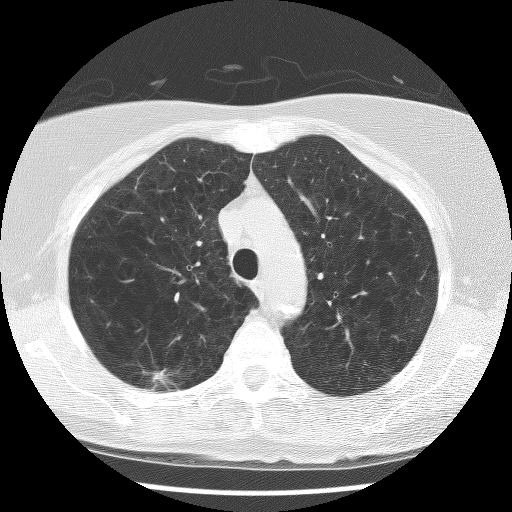
Chest CT (low-dose screening protocol), one axial image, first (baseline) screen, lung window (W 1500 / L -600 HU), 2.5 mm slice thickness, lung (sharp) reconstruction kernel (BONE), 120 kVp, 512 × 512 image matrix, field of view 310 × 310 mm. Female participant, aged 63 years at enrolment.
Expert-annotated lung lesion, bounding box <130,353,190,403> (left, top, right, bottom; pixels). The exam's reader record, not a measurement of the box and not confirmed to be the same lesion: non-calcified nodule or mass ≥4 mm, right upper lobe, 9 × 6 mm, spiculated (stellate) margins, mixed attenuation. Lung cancer was diagnosed 350 days after this screen: bronchiolo-alveolar carcinoma, non-mucinous, right upper lobe, well differentiated (G1), stage IA (AJCC 6th edition), 12 mm at pathology.